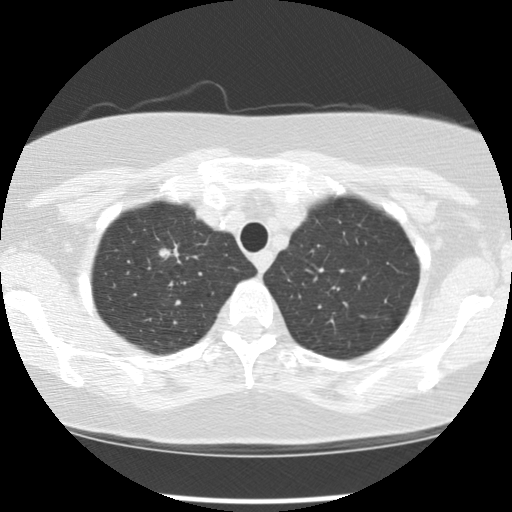
Low-dose screening chest CT, axial slice. First (baseline) screen. Lung window (W 1500 / L -600 HU). 2.5 mm slice thickness. 120 kVp. Female, age 65 years at enrolment.
Expert reader's lesion annotation, bounding box [x1, y1, x2, y2] px = [147, 231, 196, 280]. The screening reader recorded 2 non-calcified nodules or masses ≥4 mm on this exam; which of them this box marks is not recorded. Official screen result: positive, change unspecified: nodule(s) >= 4 mm or enlarging nodule(s), mass(es), or other non-specific abnormalities suspicious for lung cancer. Participant outcome: lung cancer diagnosed 183 days after this screen — large cell carcinoma, NOS, right upper lobe, poorly differentiated (G3), stage IA (AJCC 6th edition), 20 mm at pathology.